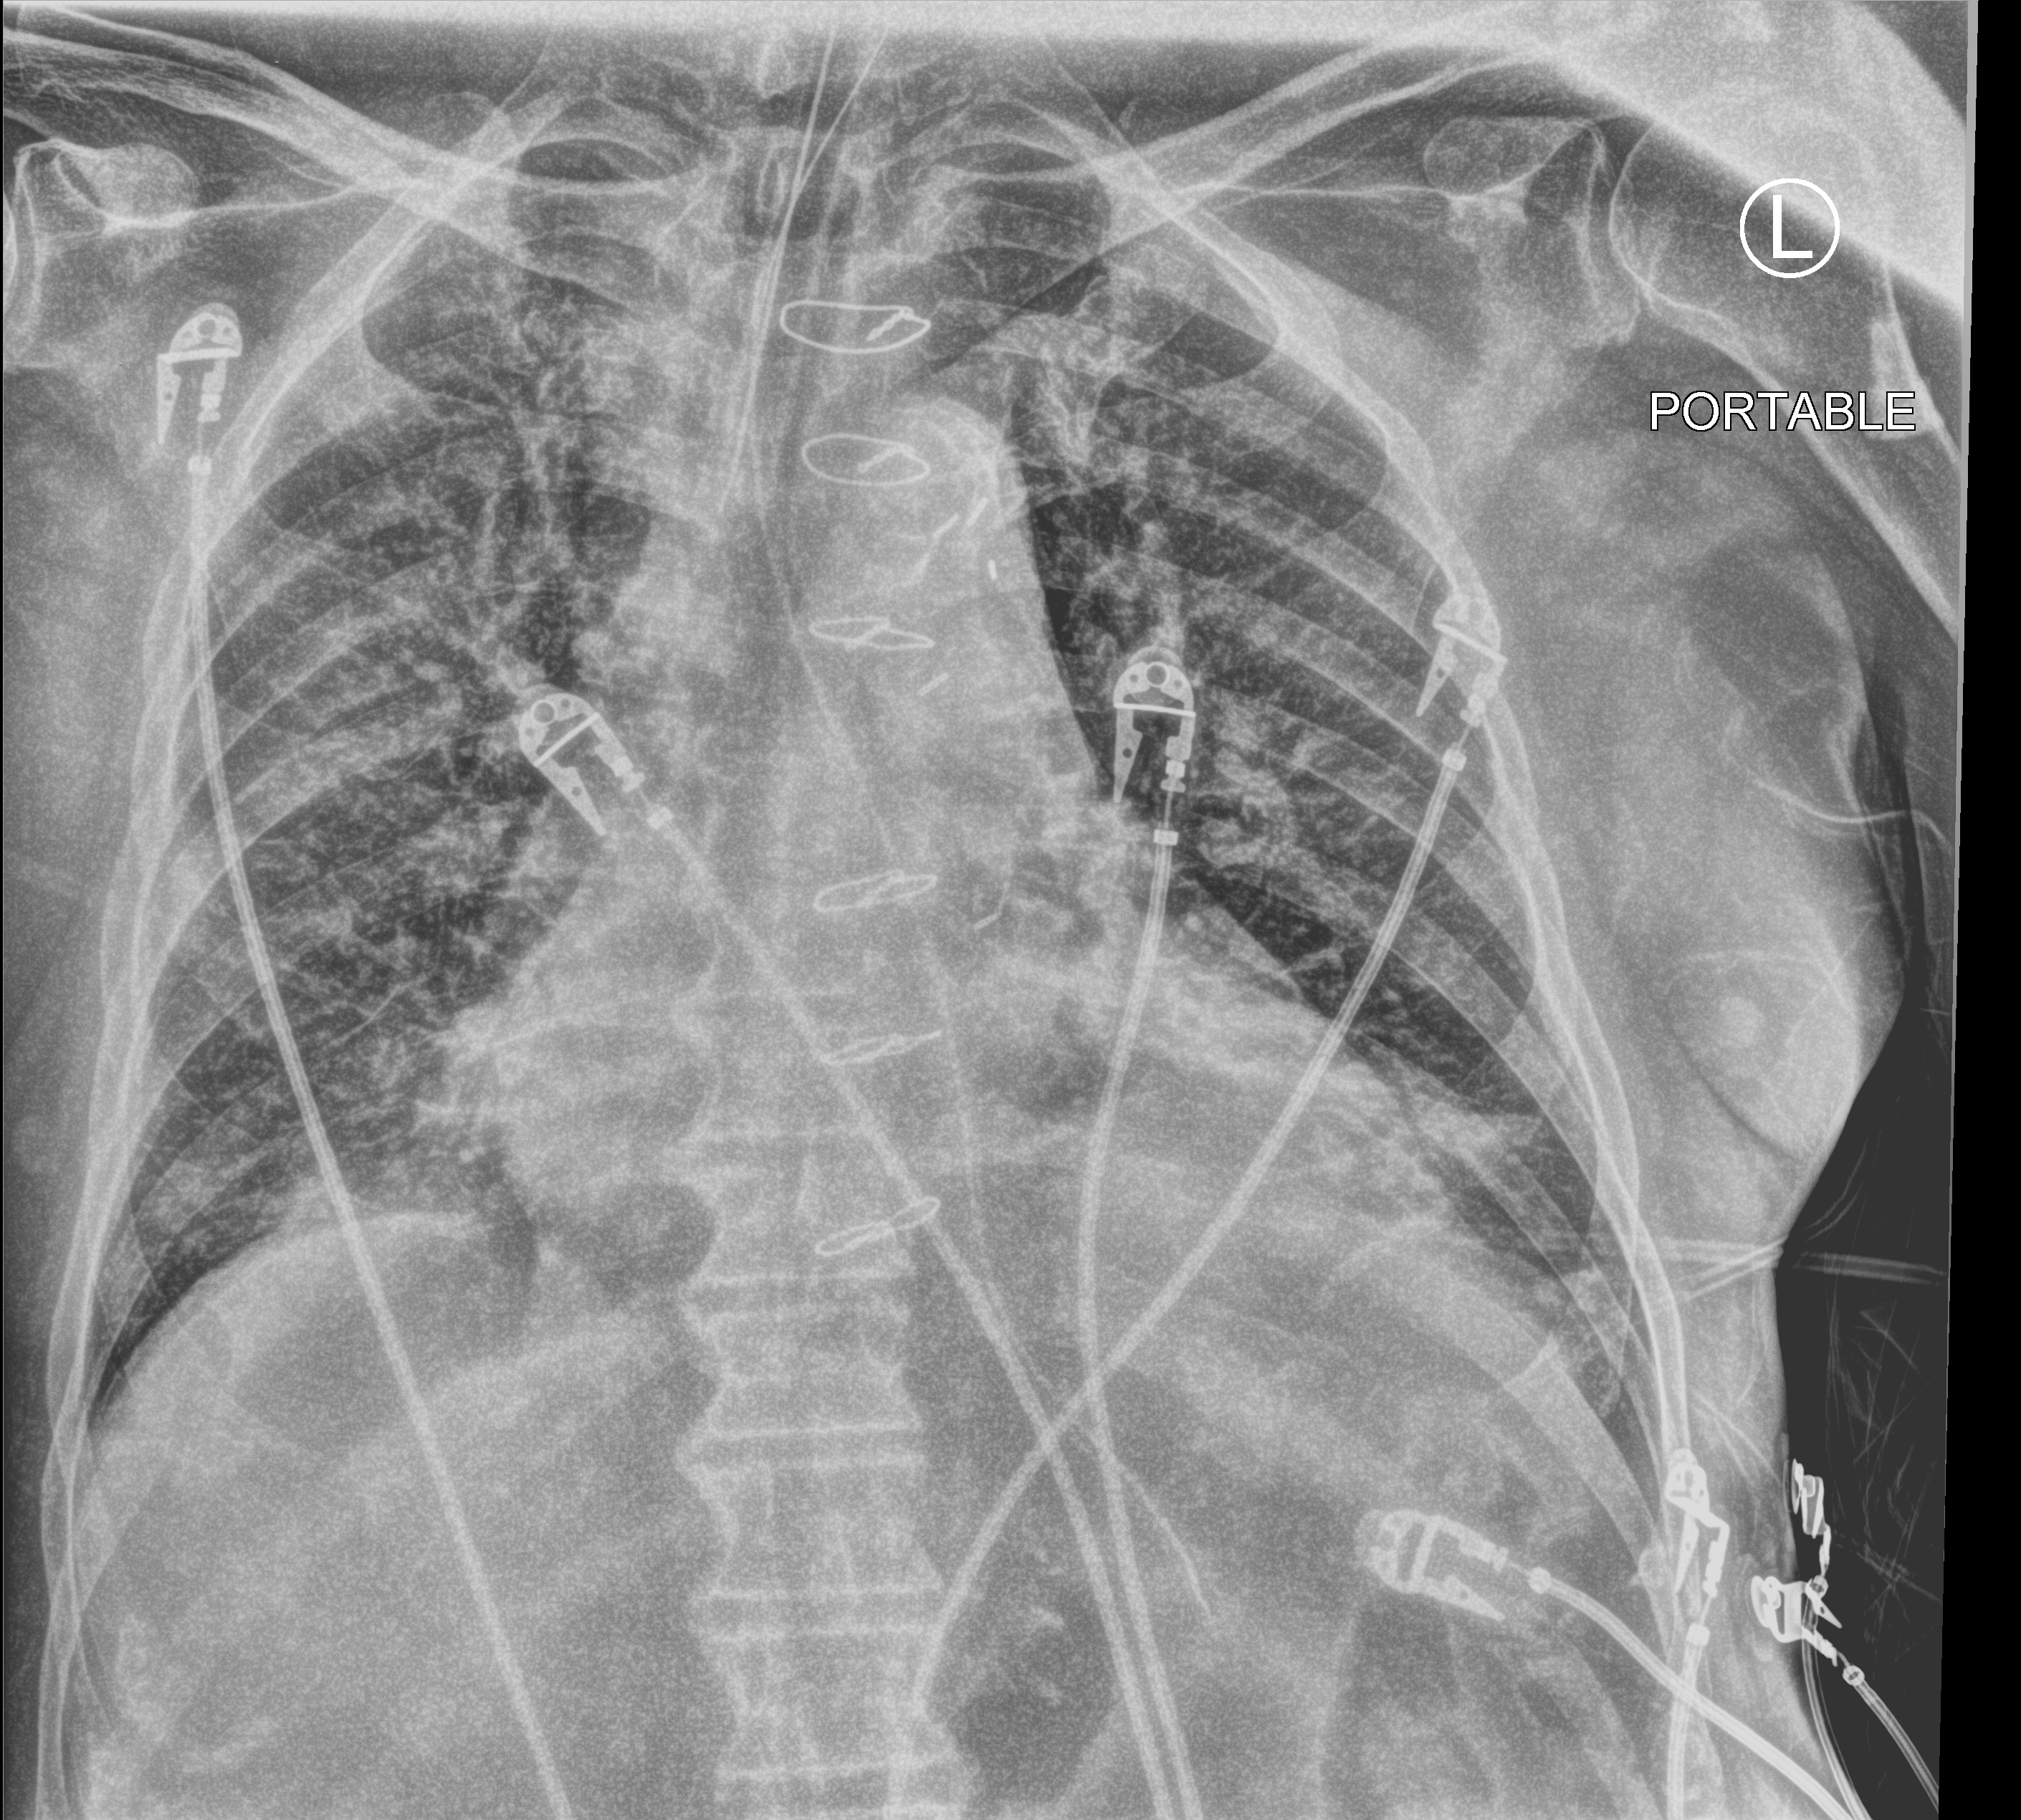
Portable chest radiograph, anteroposterior (AP) projection. Male patient hospitalised with COVID-19, age 75–90 years.
From the hospital-stay record, not from the radiograph (when in the stay this image was taken is not recorded): admitted to intensive care during this hospital stay: yes; mechanically ventilated during this hospital stay: yes.